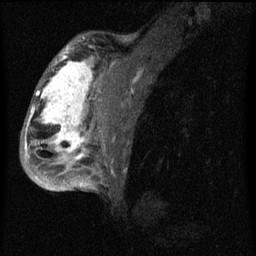
Breast MRI (dynamic contrast-enhanced), one sagittal slice; position 42 of 60 along the scan axis; dynamic contrast-enhanced series, image 2 of 4 at this slice position (ordered by acquisition); 1.5 T; TE 4.2 ms, TR 8 ms; 2 mm slice thickness; 256 × 256 image matrix, field of view 180 × 180 mm. Female patient, age 50 years.
Annotated regions visible in this slice (semi-automatically segmented with operator editing):
- analysis volume of interest (the breast-tissue region the enhancement analysis was run in; not a lesion): bounding box (x1, y1, x2, y2) in pixels: (26, 44, 124, 177)
- tumour enhancement mask (voxels above the 70 % enhancement threshold inside the analysis volume of interest): (26, 46, 94, 161)